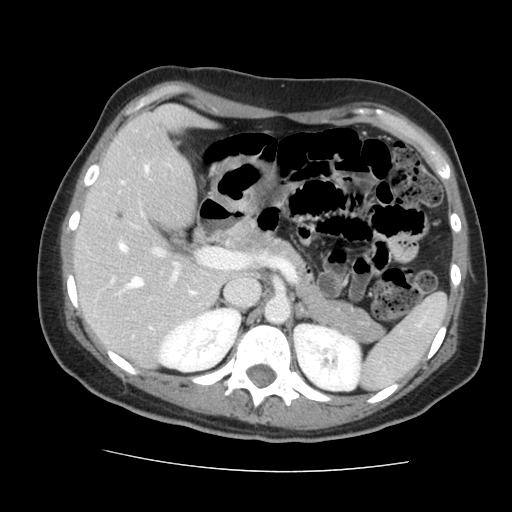
Contrast-enhanced abdominal CT, one axial slice. Slice 90 of 144 in the series (ordered by position). 120 kVp. Intravenous contrast given. Soft-tissue window (W 400 / L 40 HU). 2.5 mm slice thickness. 512 × 512 image matrix, field of view 333 × 333 mm. Female patient, age 46 years. Case-level facts recorded for this patient, not image findings: diagnosis: colorectal cancer liver metastases, imaged before liver resection; multiple liver metastases: no; largest metastasis: 2.8 cm; disease in both lobes: no.
Annotated regions visible in this slice (manually delineated by an expert):
- hepatic veins: bounding box <121,165,194,294> (left, top, right, bottom; pixels)
- liver: <78,108,221,365>
- planned liver remnant (the part of the liver to remain after resection): <78,108,221,365>
- portal vein (with intrahepatic branches): <119,225,226,281>
- liver metastasis: <118,214,123,219>